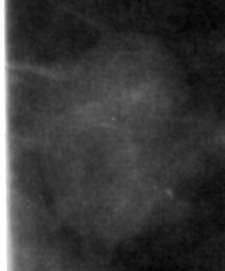
Region of interest cut from a scanned film mammogram (one marked finding), right breast, CC view, BI-RADS breast density category 3 (scale 1–4).
Marked abnormality: mass, shape lobulated, margins obscured; BI-RADS assessment category 3; pathology (as recorded): benign.